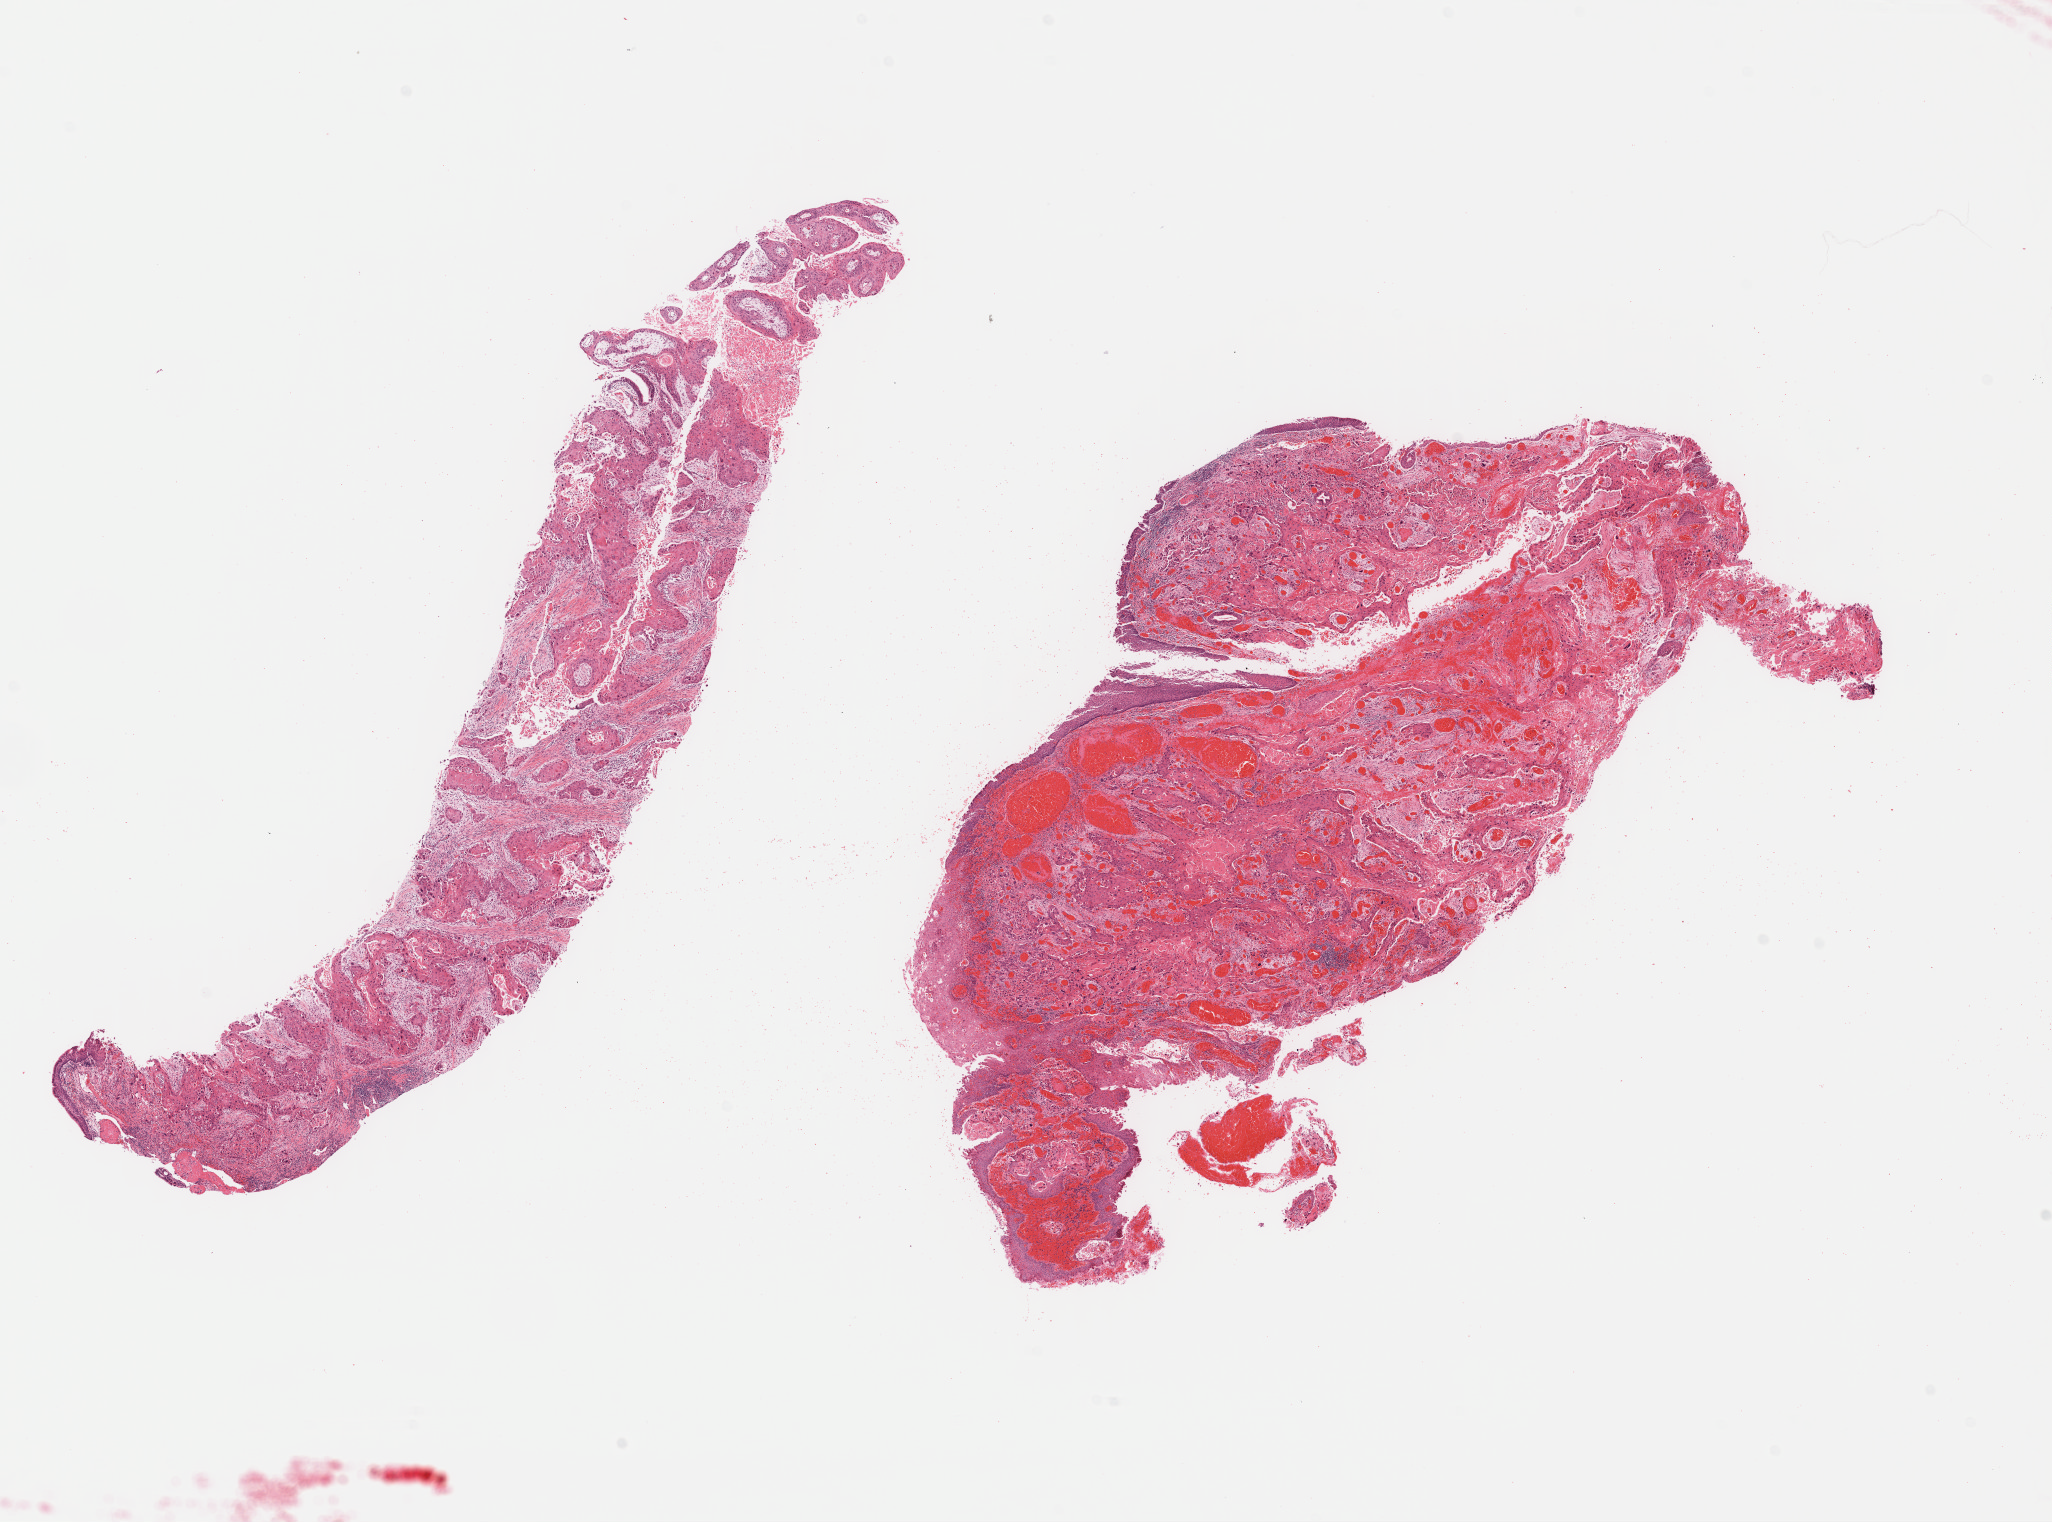
Whole-slide histology image, H&E, low-resolution overview of the scanned area, about 16.1 x 12.0 mm (from a 40x scan), formalin-fixed paraffin-embedded (FFPE) diagnostic section, sample: primary tumour, head and neck. Male, age 72 years at initial diagnosis. Histologic grade: G2 (moderately differentiated).
TNM: T4a N0 M0. Histologic diagnosis: Squamous cell carcinoma, NOS (larynx, NOS). AJCC pathologic stage: IVA.